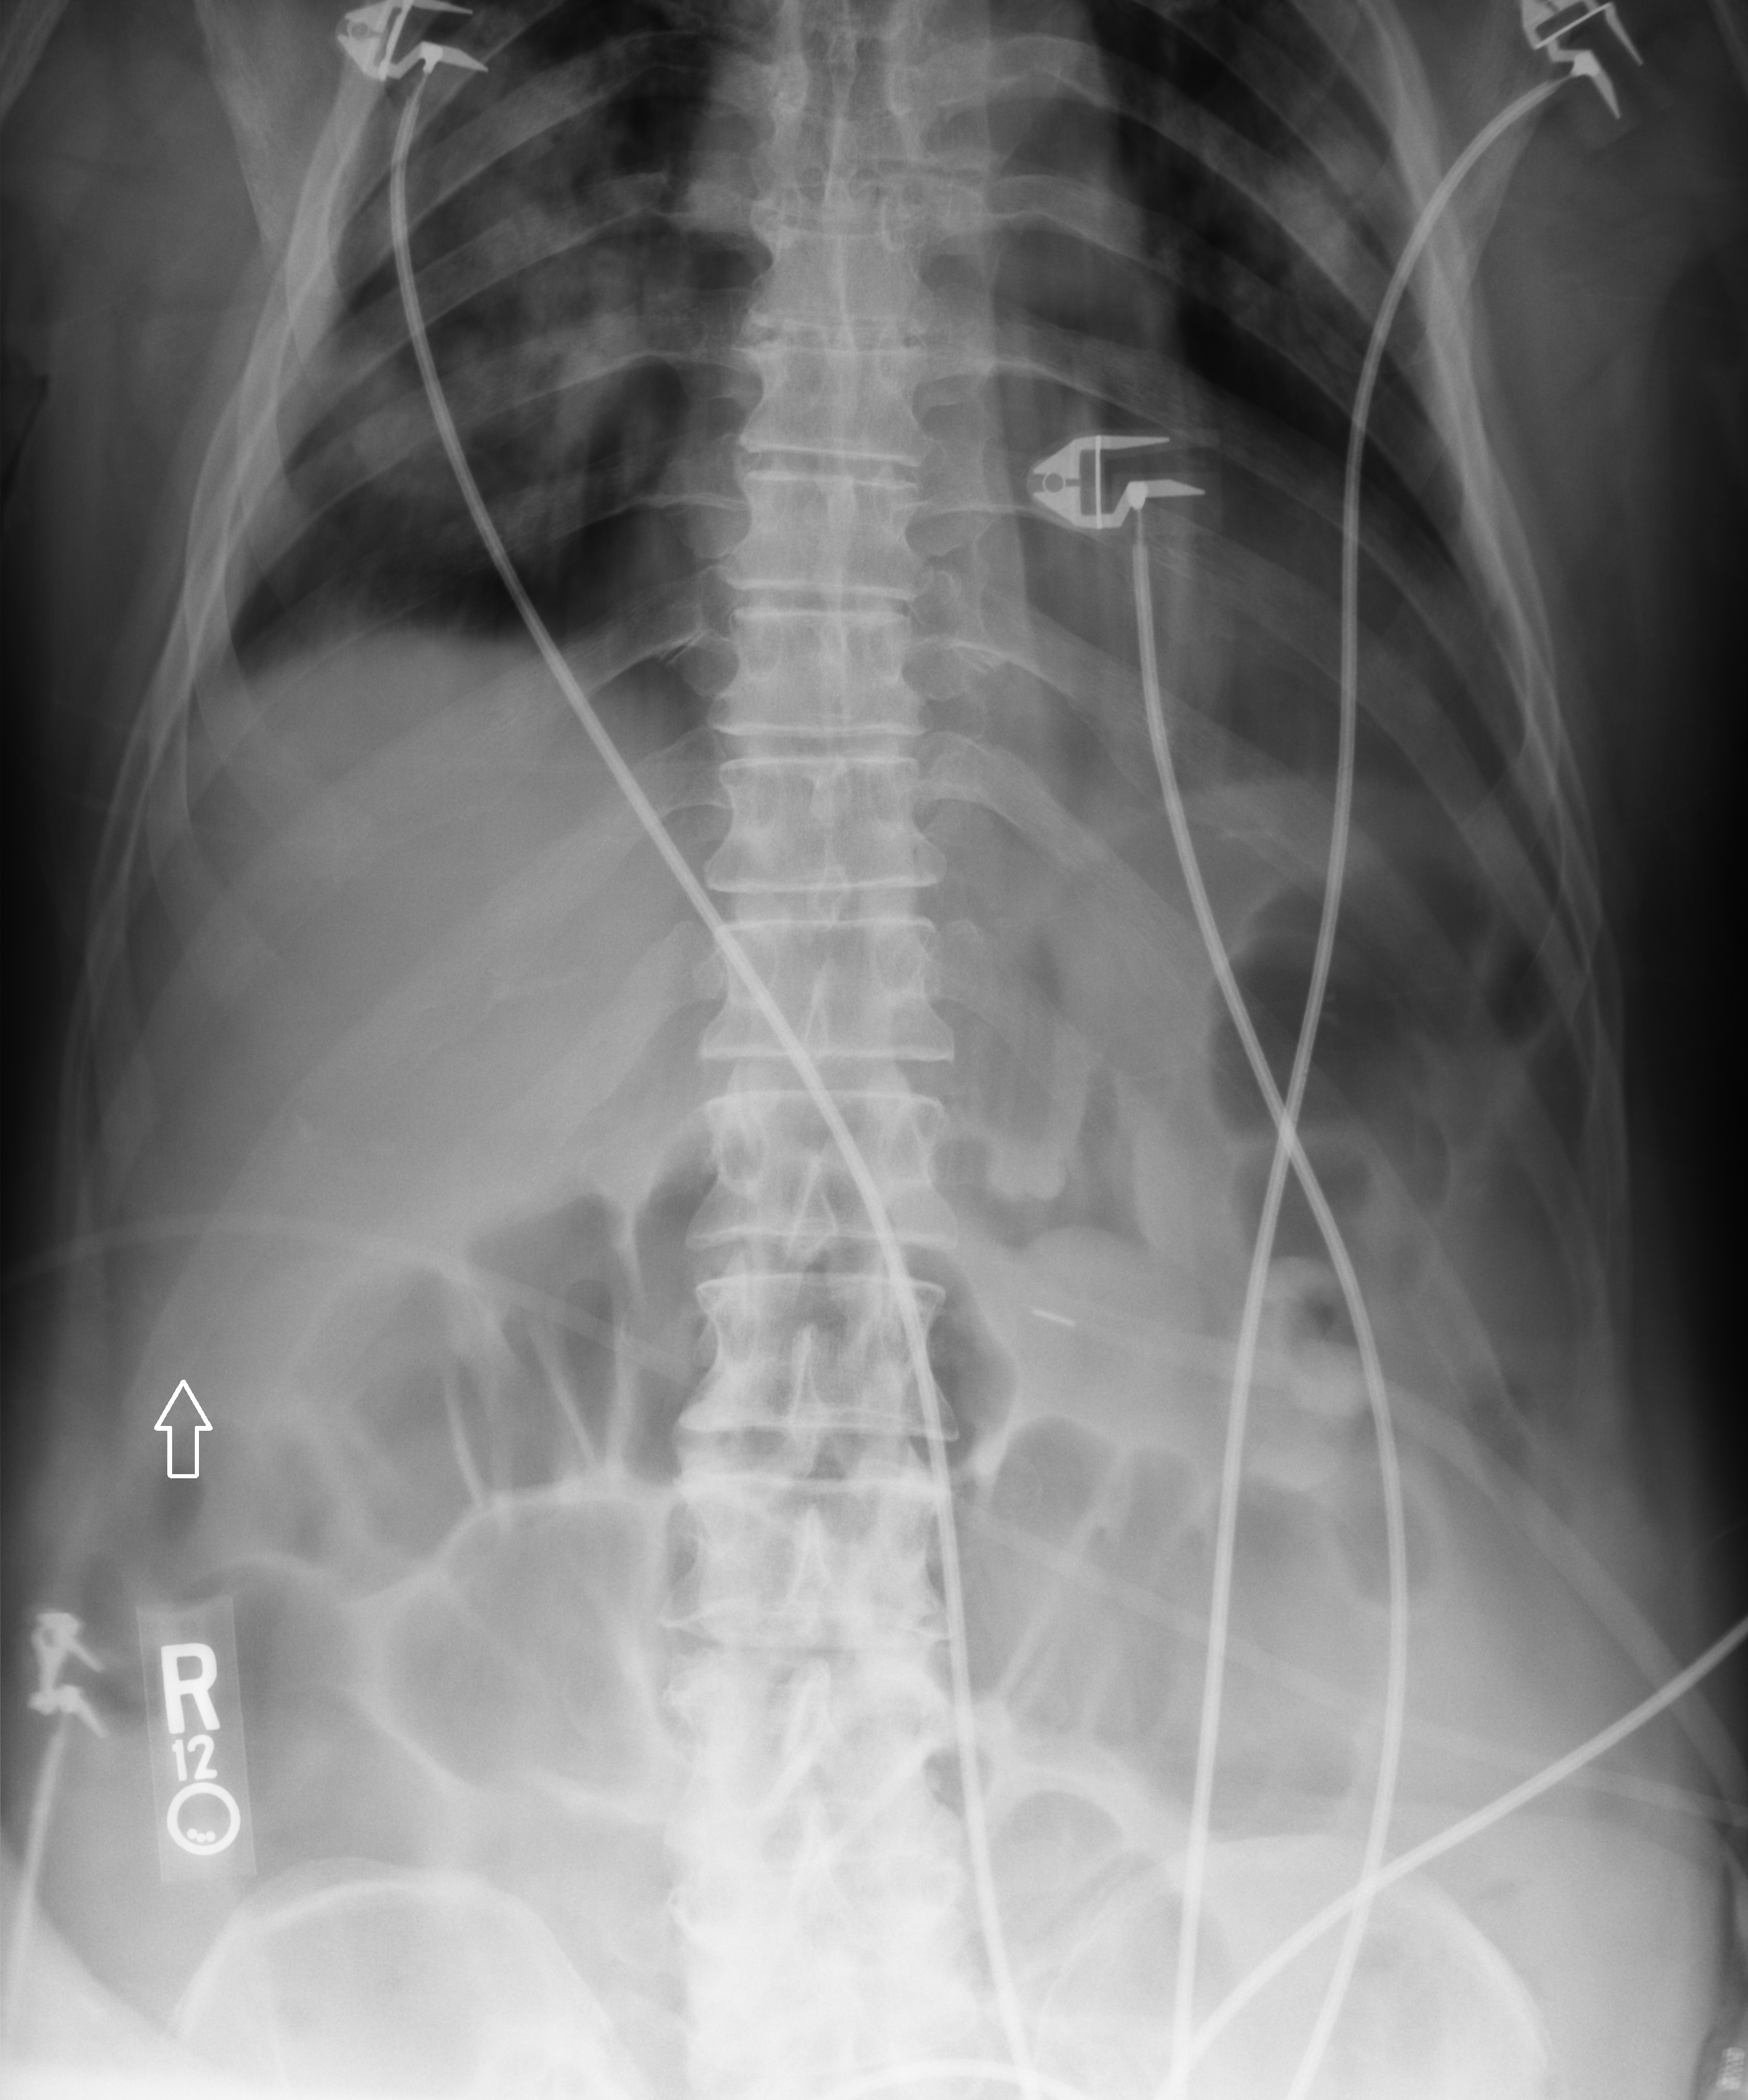
Bedside abdomen radiograph (computed radiography), anteroposterior (AP) projection. Male patient hospitalised with COVID-19, age 60–74 years.
Admission-level facts for this patient (not findings on this image; timing relative to this image not recorded):
- mechanically ventilated during this hospital stay: no
- admitted to intensive care during this hospital stay: no